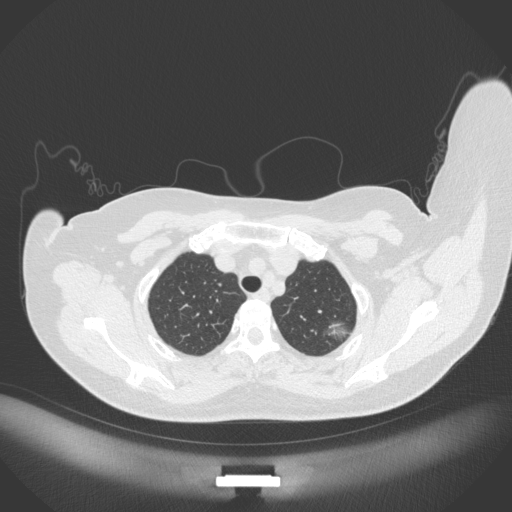
Chest CT, one axial slice; position 312 of 386 along the scan axis; reconstruction kernel B31f; 120 kVp; lung window (W 1500 / L -600 HU); 1 mm slice thickness; 512 × 512 image matrix. Female patient, age 58 years. From the clinical record (not read from this slice): clinical TNM (as recorded): T1c N0 M0.
Annotated regions visible in this slice (rectangle marked by the reading radiologist):
- lung tumour (recorded histology: adenocarcinoma): bounding box (x1, y1, x2, y2) in pixels: (324, 323, 348, 339)